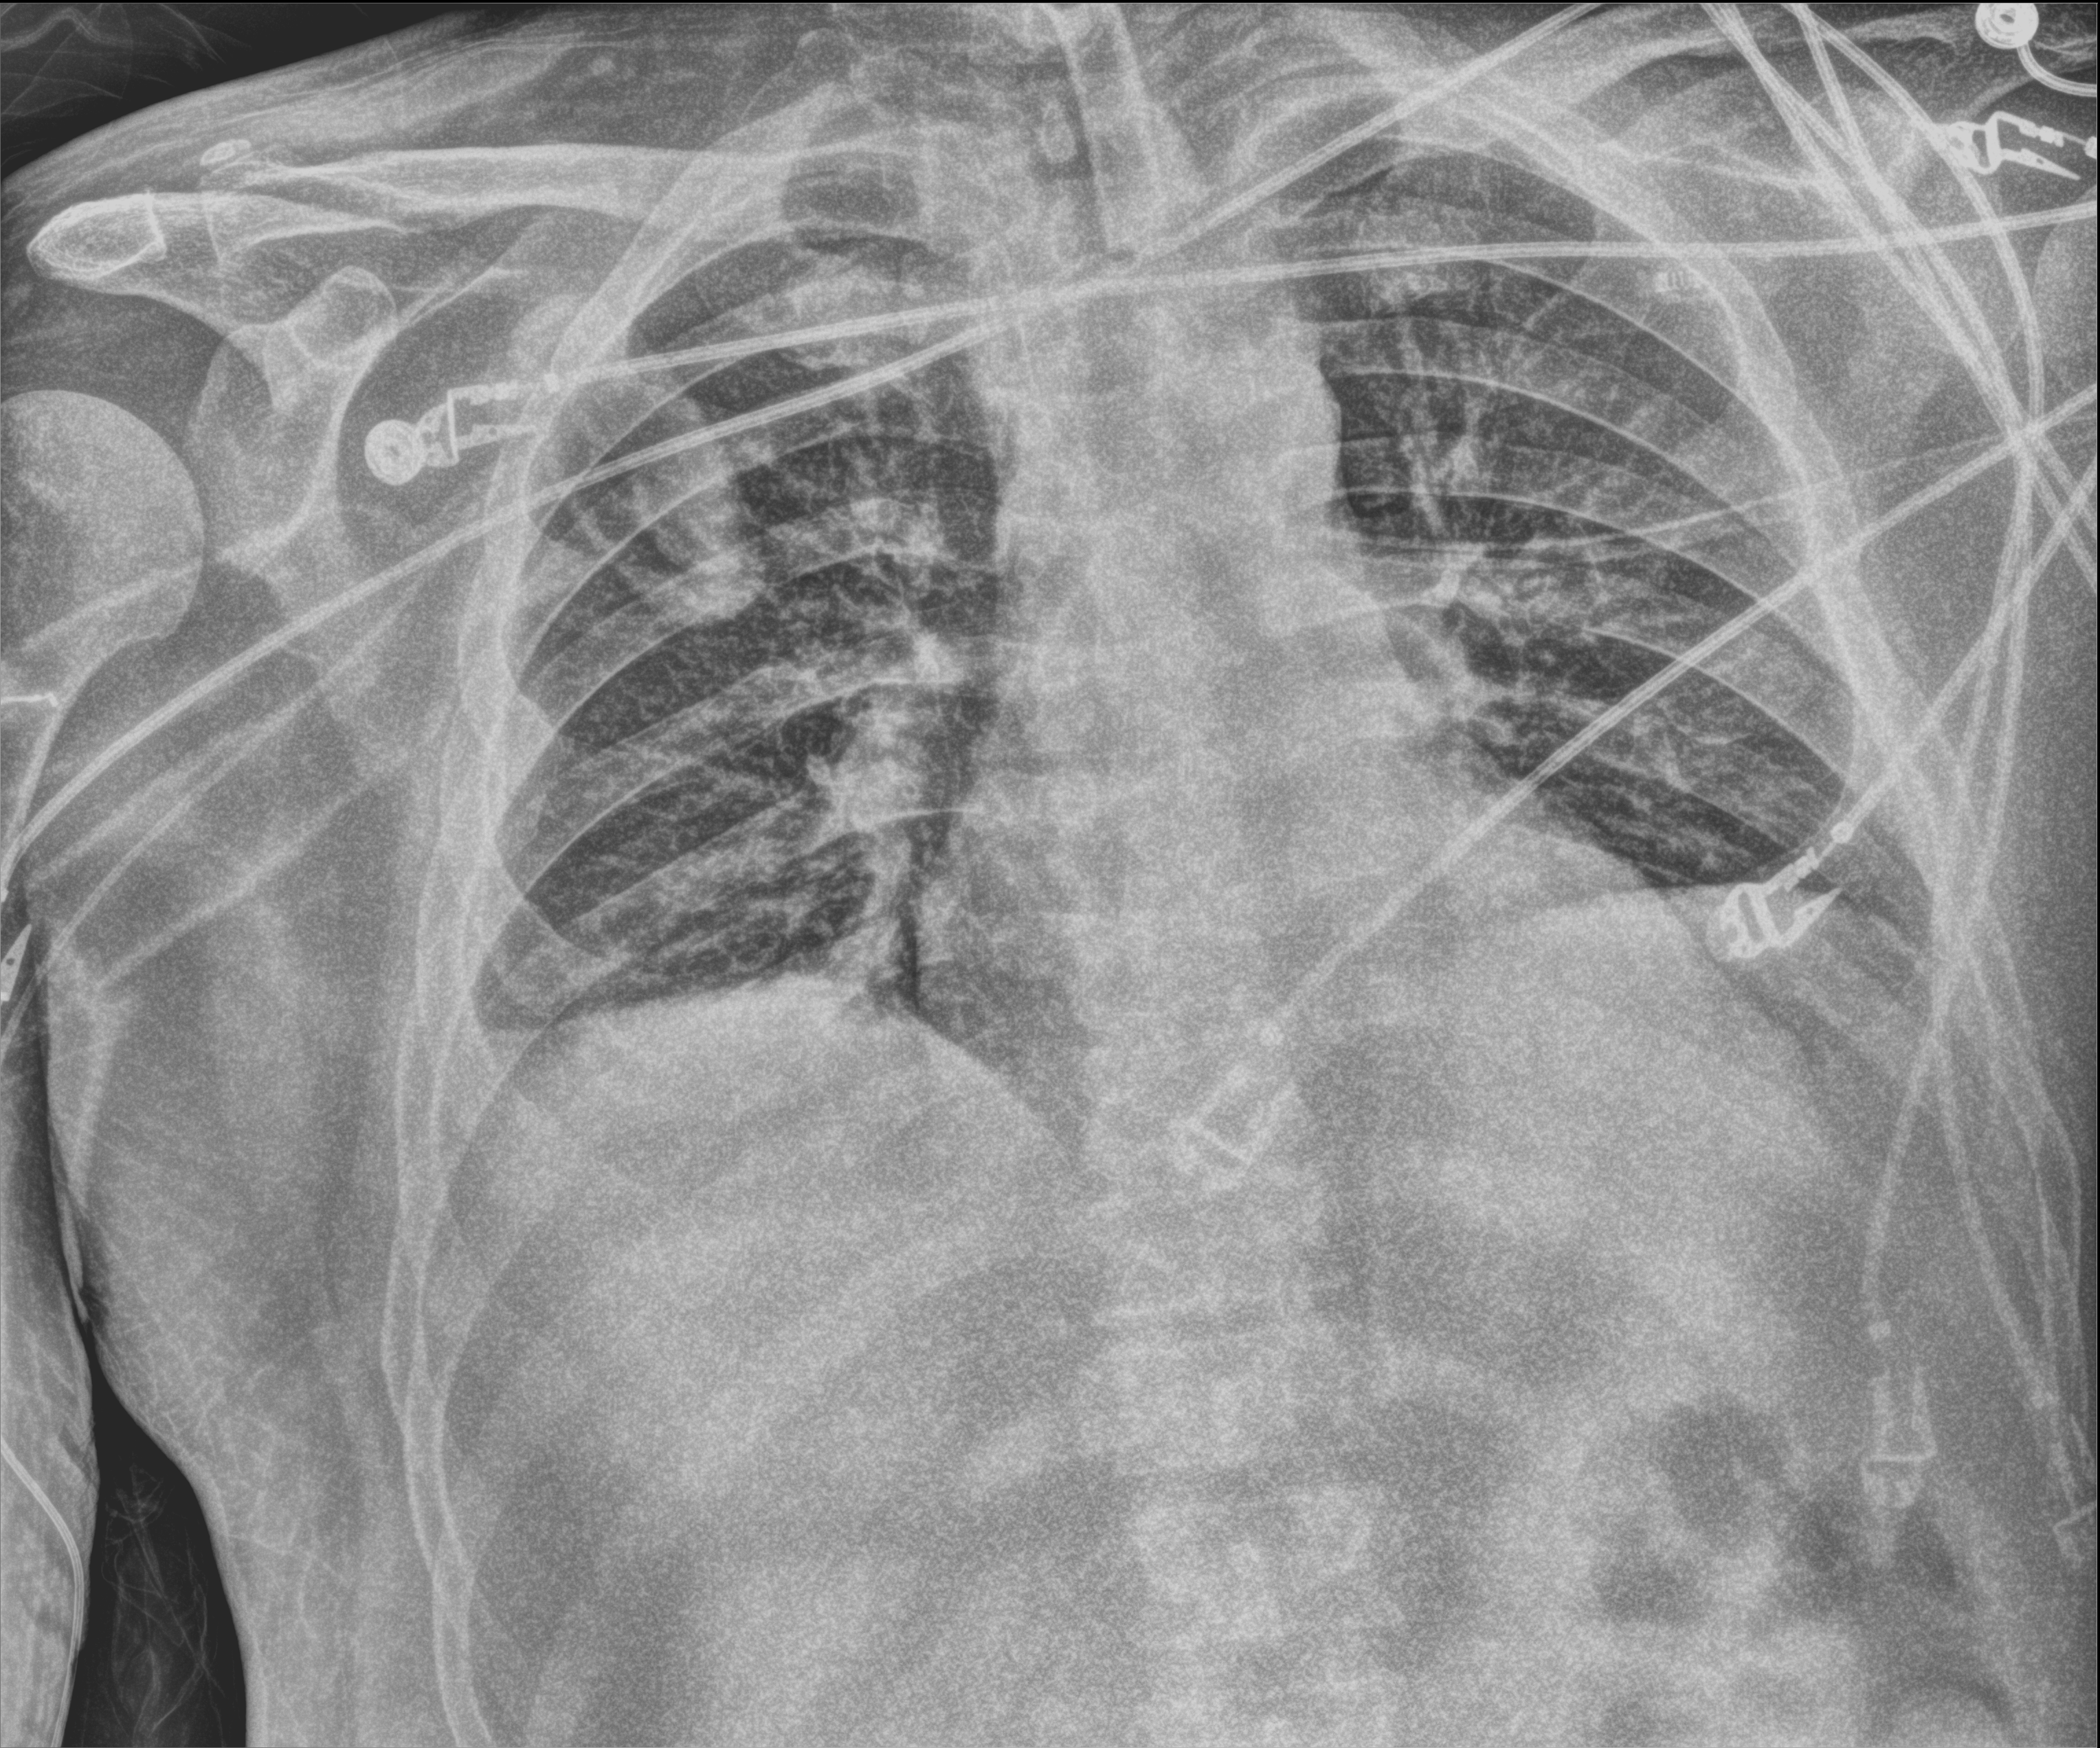
Portable chest radiograph, anteroposterior (AP) projection. Male patient hospitalised with COVID-19, age 18–59 years.
From the hospital-stay record, not from the radiograph (when in the stay this image was taken is not recorded): mechanically ventilated during this hospital stay: yes; admitted to intensive care during this hospital stay: yes.